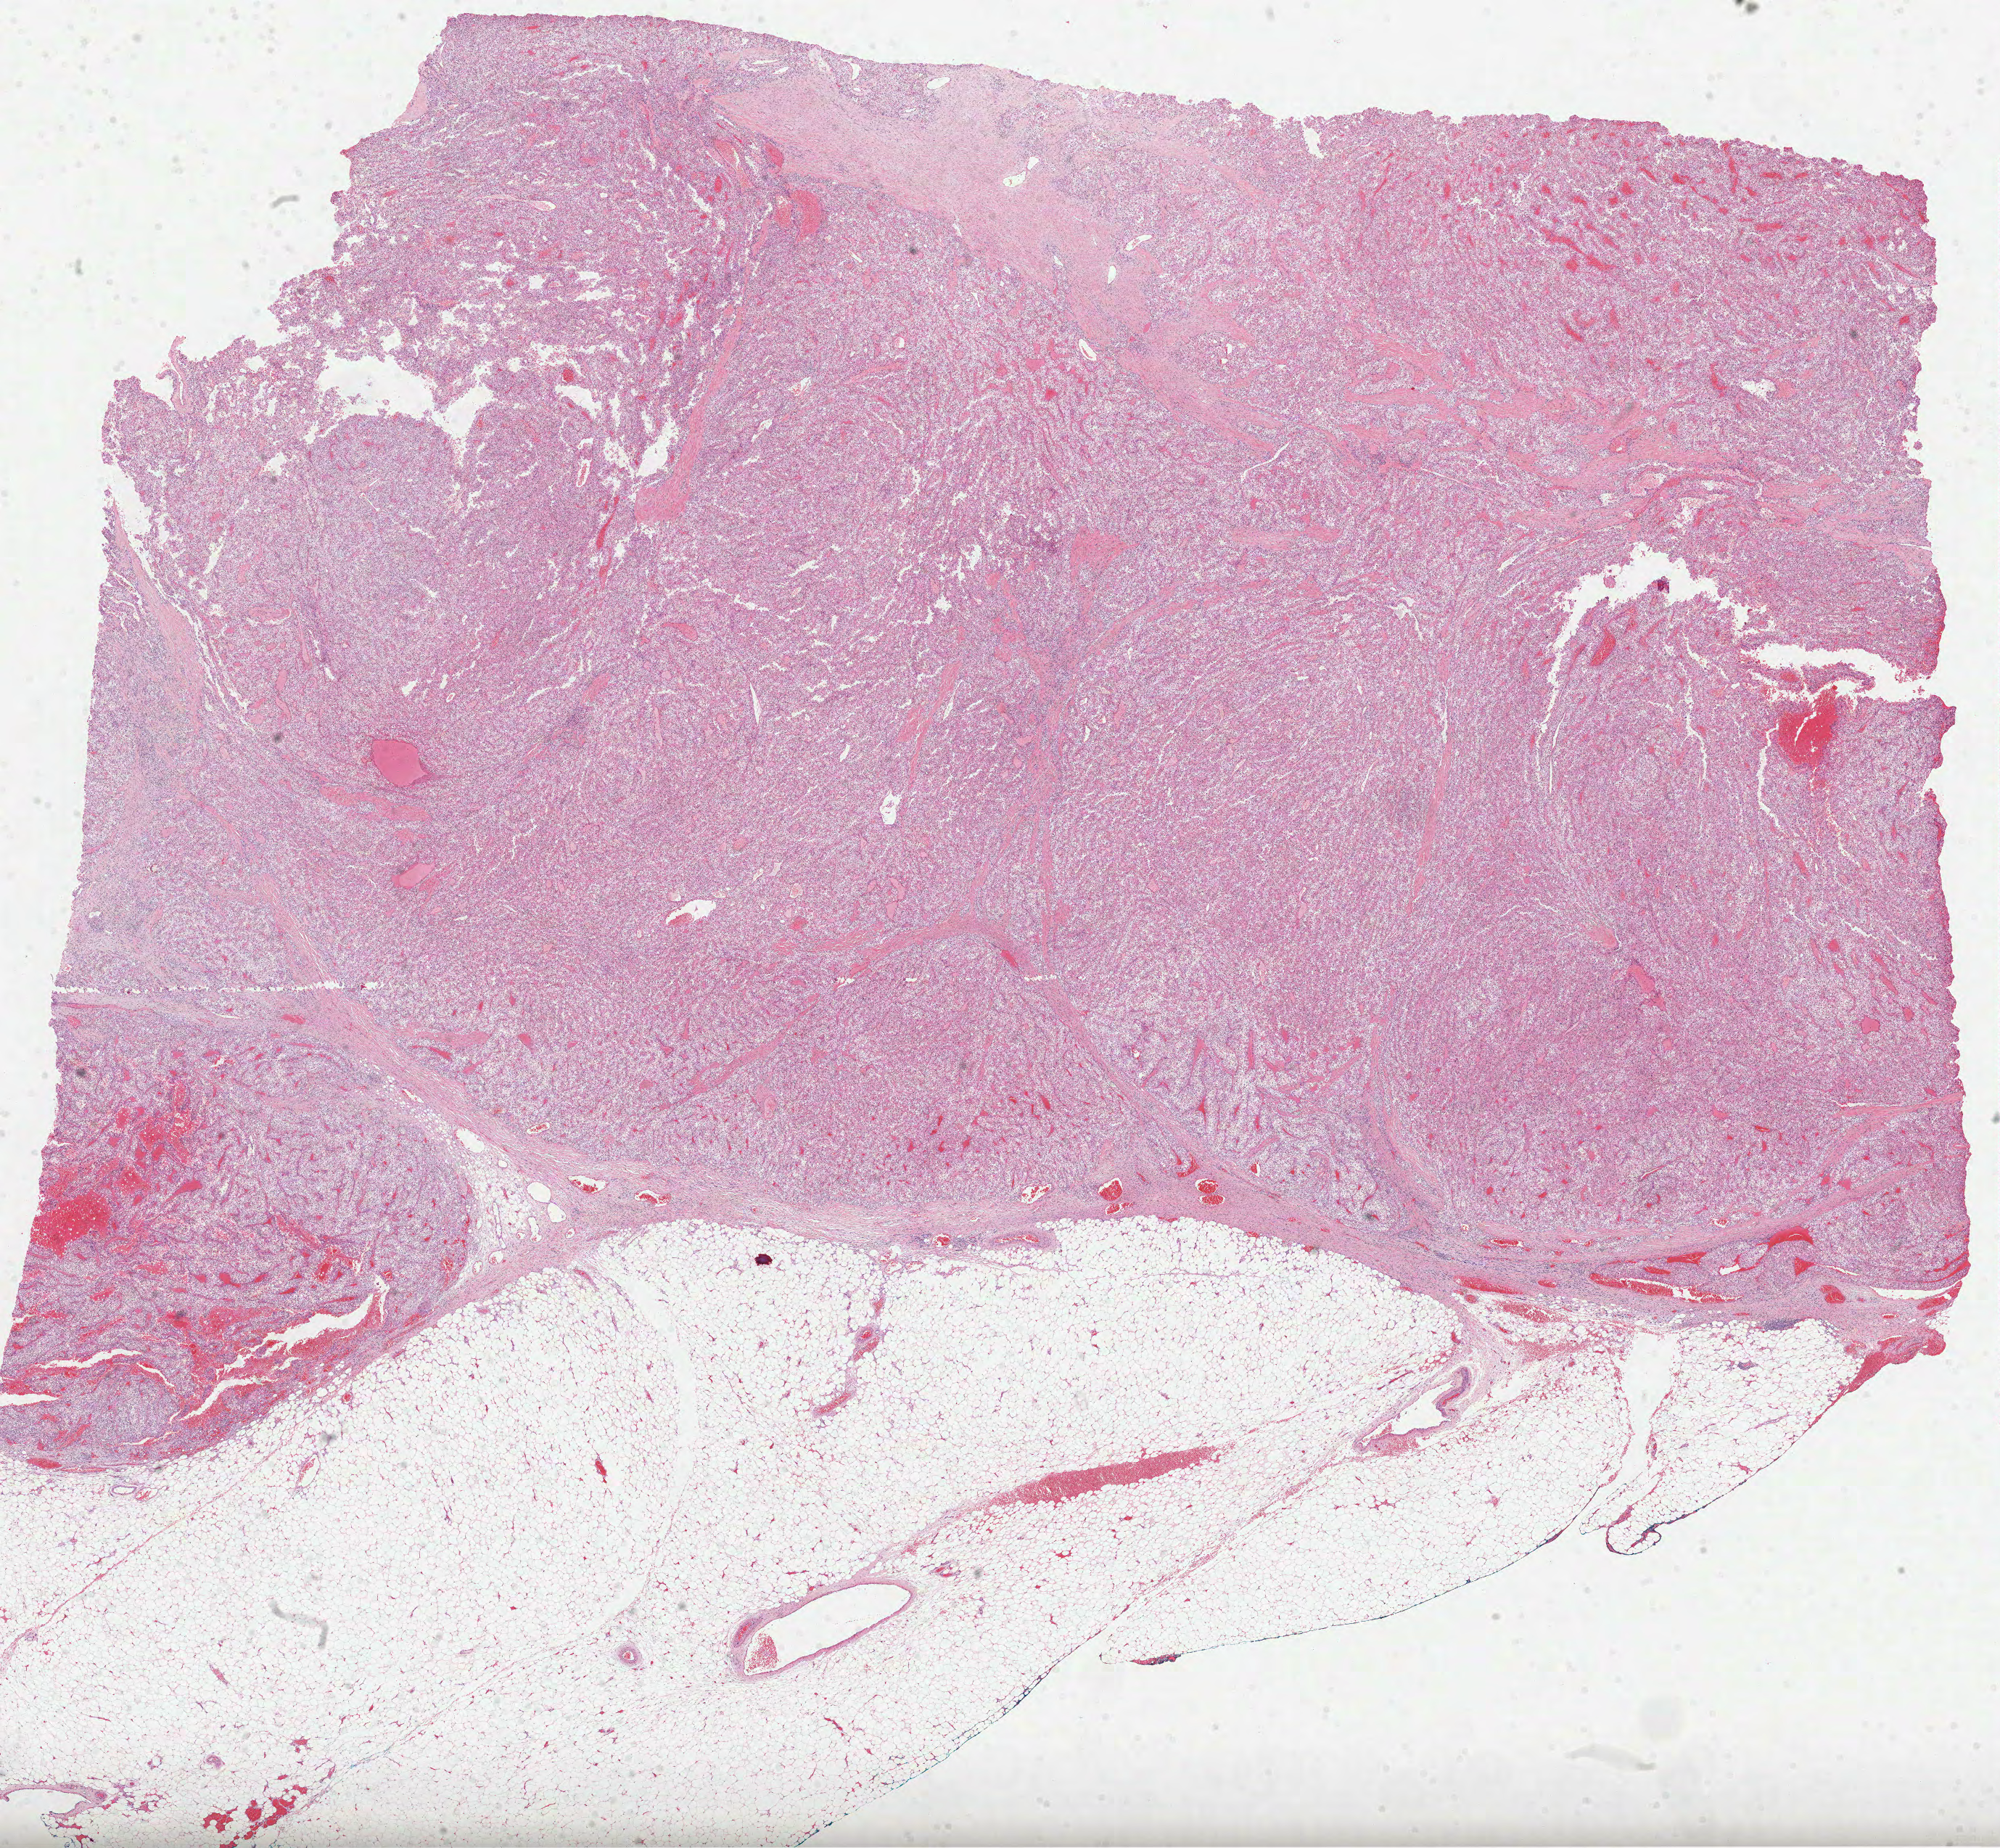
Whole-slide histology image, H&E-stained, shown as a low-resolution overview of the whole scanned area (about 22.2 x 20.5 mm, from a 40x scan); formalin-fixed paraffin-embedded (FFPE) diagnostic section; kidney, primary tumour sample. Patient: female, age at initial diagnosis 76 years. Histologic grade: G2 (moderately differentiated).
AJCC pathologic stage: III. Pathologic diagnosis: Clear cell adenocarcinoma, NOS.